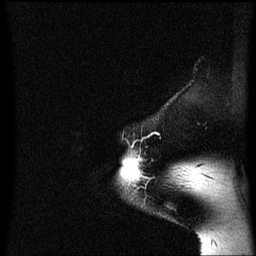
Breast MRI (dynamic contrast-enhanced), one sagittal slice; slice 55 of 60 in the series (ordered by position); dynamic contrast-enhanced series, image 2 of 3 at this slice position (ordered by acquisition); 1.5 T; TE 4.2 ms, TR 8.4 ms; 256 × 256 image matrix, field of view 200 × 200 mm. Female patient, age 54 years. Case-level facts recorded for this patient, not image findings: setting: breast cancer imaged before/during neoadjuvant chemotherapy; receptor status: HR-positive, HER2-negative.
Outlined on this slice (semi-automatically segmented with operator editing):
- analysis volume of interest (the breast-tissue region the enhancement analysis was run in; not a lesion): box from (x=123, y=156) to (x=144, y=183) px
- tumour enhancement mask (voxels above the 70 % enhancement threshold inside the analysis volume of interest): (x=123, y=158)–(x=144, y=183)